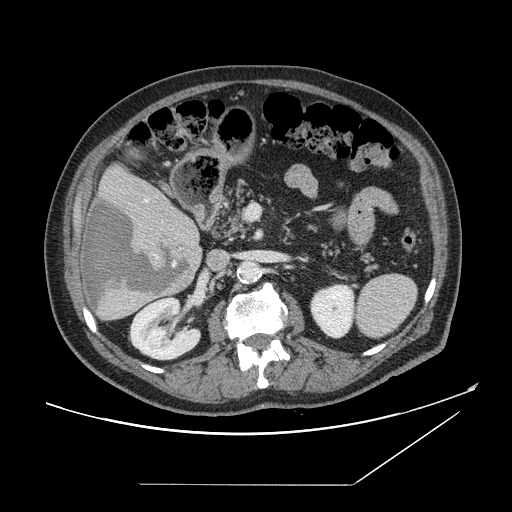
Contrast-enhanced abdominal CT, one axial slice; slice 74 of 166 in the series (ordered by position); 120 kVp; soft-tissue window (W 400 / L 40 HU); 2.5 mm slice thickness; 512 × 512 image matrix, field of view 416 × 416 mm. Male patient, age 80 years. Case-level facts recorded for this patient, not image findings: diagnosis: colorectal cancer liver metastases, imaged before liver resection; multiple liver metastases: no; largest metastasis: 2.2 cm; chemotherapy before resection: no.
Annotated regions visible in this slice (outlined manually by an expert reader):
- hepatic veins: bounding box (x1, y1, x2, y2) in pixels: (146, 200, 149, 203)
- liver: (80, 164, 202, 321)
- planned liver remnant (the part of the liver to remain after resection): (103, 163, 192, 225)
- liver metastasis: (84, 199, 191, 309)